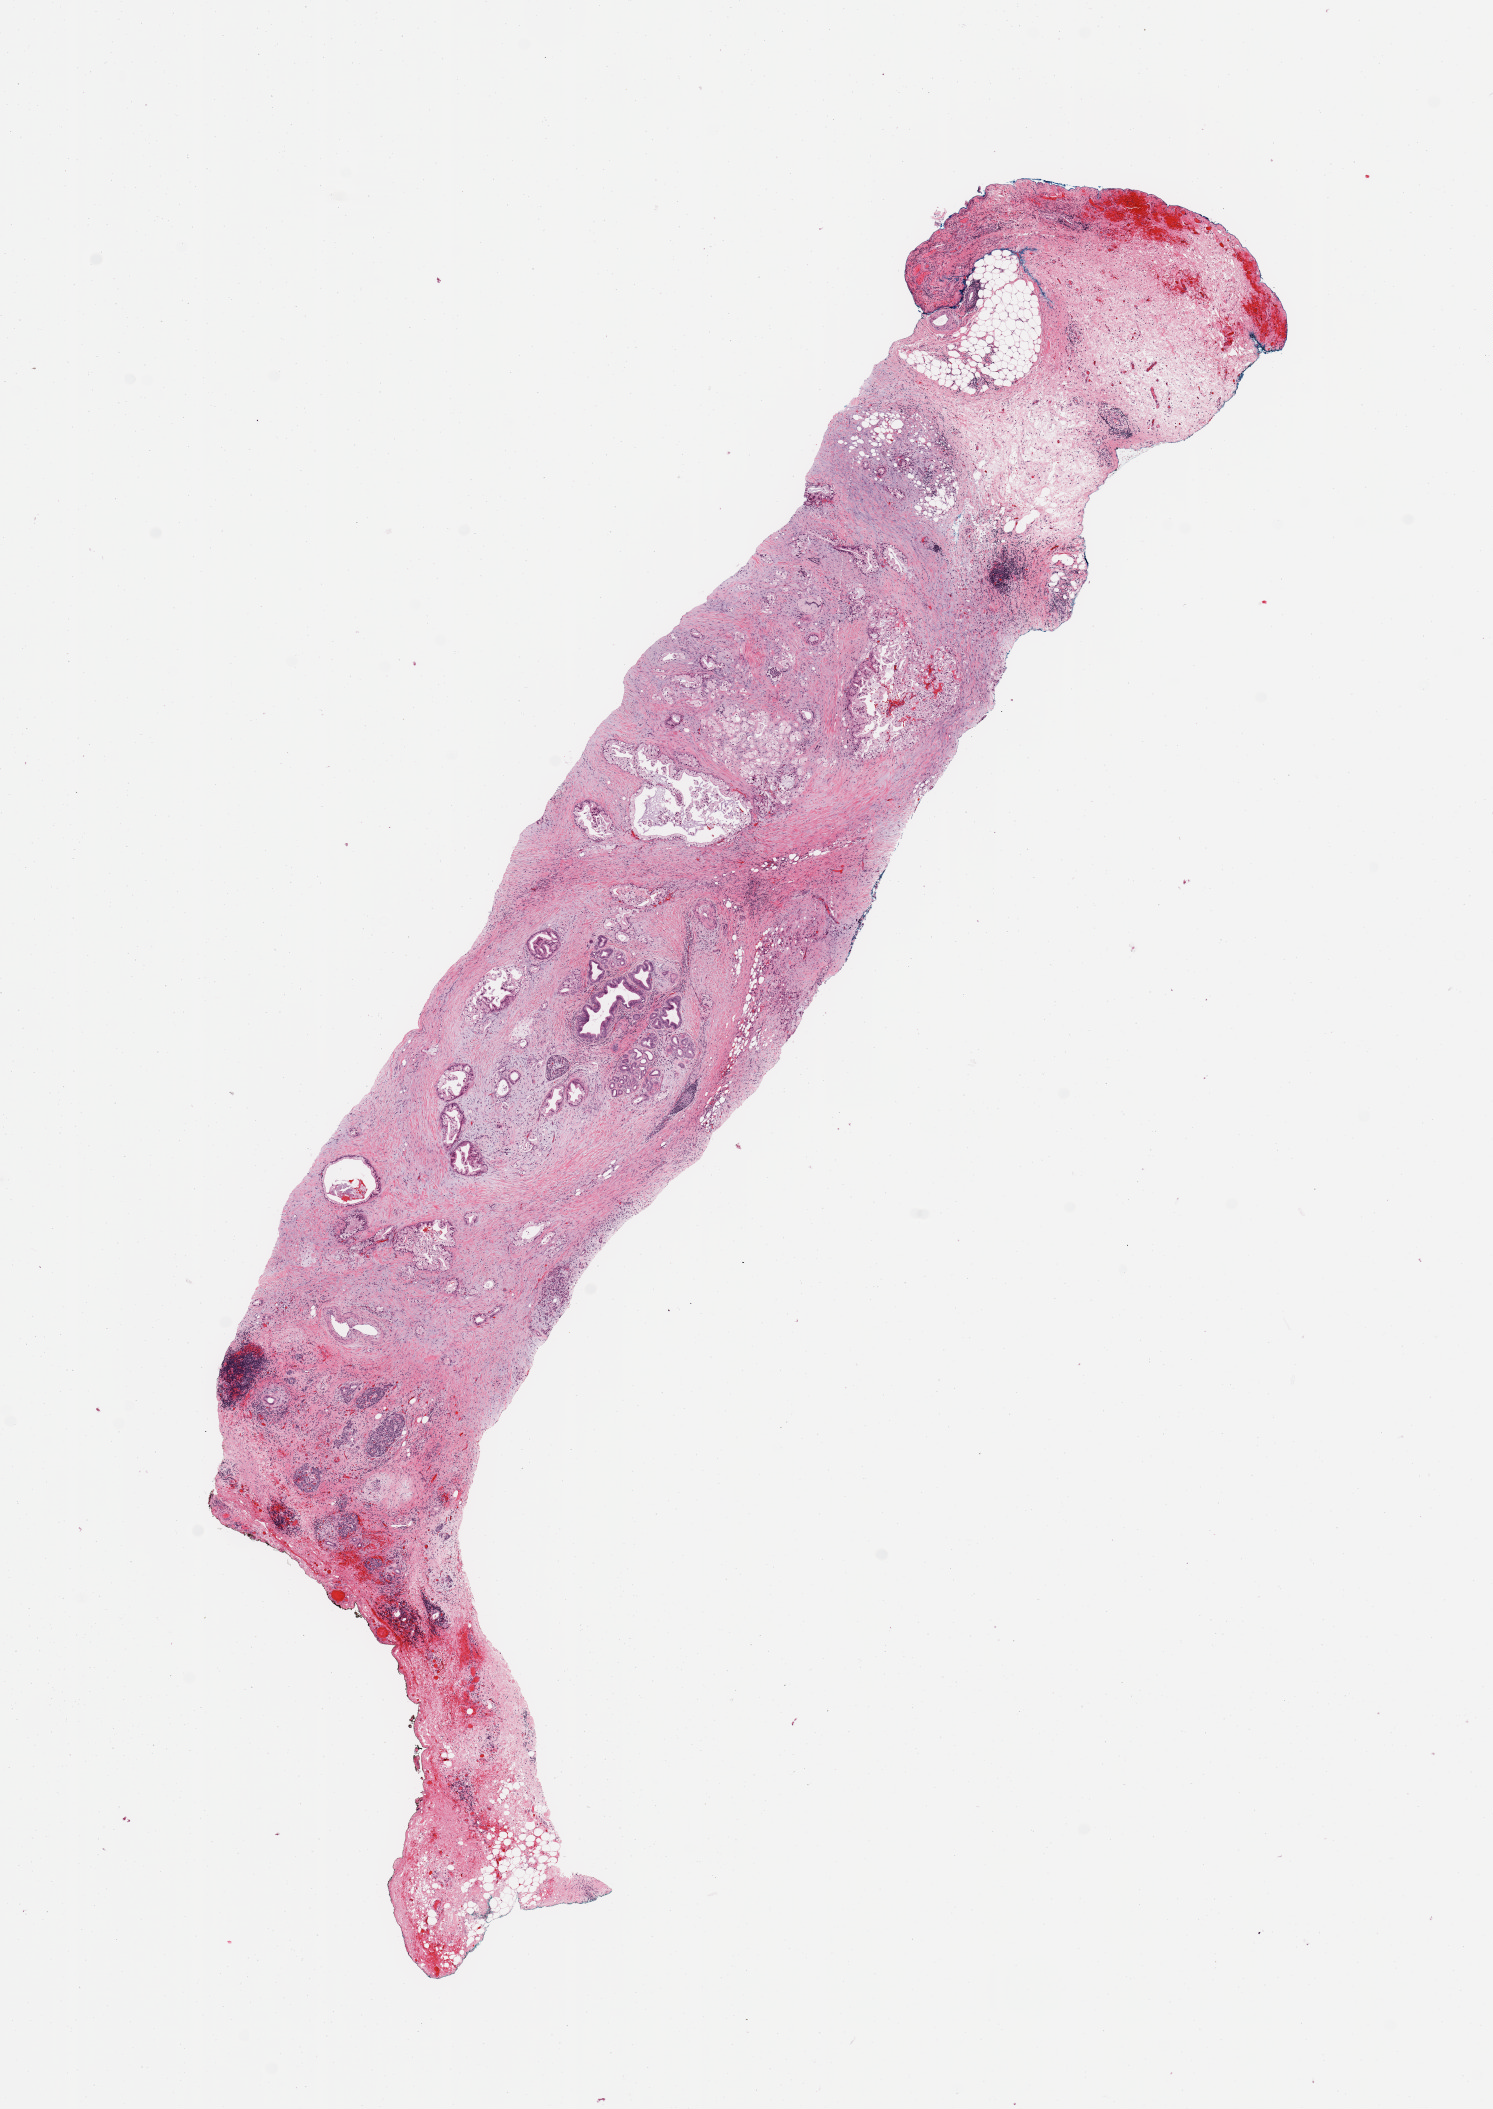
Whole-slide histology image, H&E-stained, whole scanned area (about 11.8 x 16.7 mm, acquisition: 20x scan) shown as a low-resolution overview; tumour tissue sample, sampled site: pancreas. Male, 42 y/o. Histologic grade: G3 (poorly differentiated). Composition of this section per pathologist review: tumour nuclei 20%, necrosis 0%.
AJCC pathologic stage: IIB. Primary tumour site (as recorded): head. Diagnosis: Infiltrating duct carcinoma, NOS.